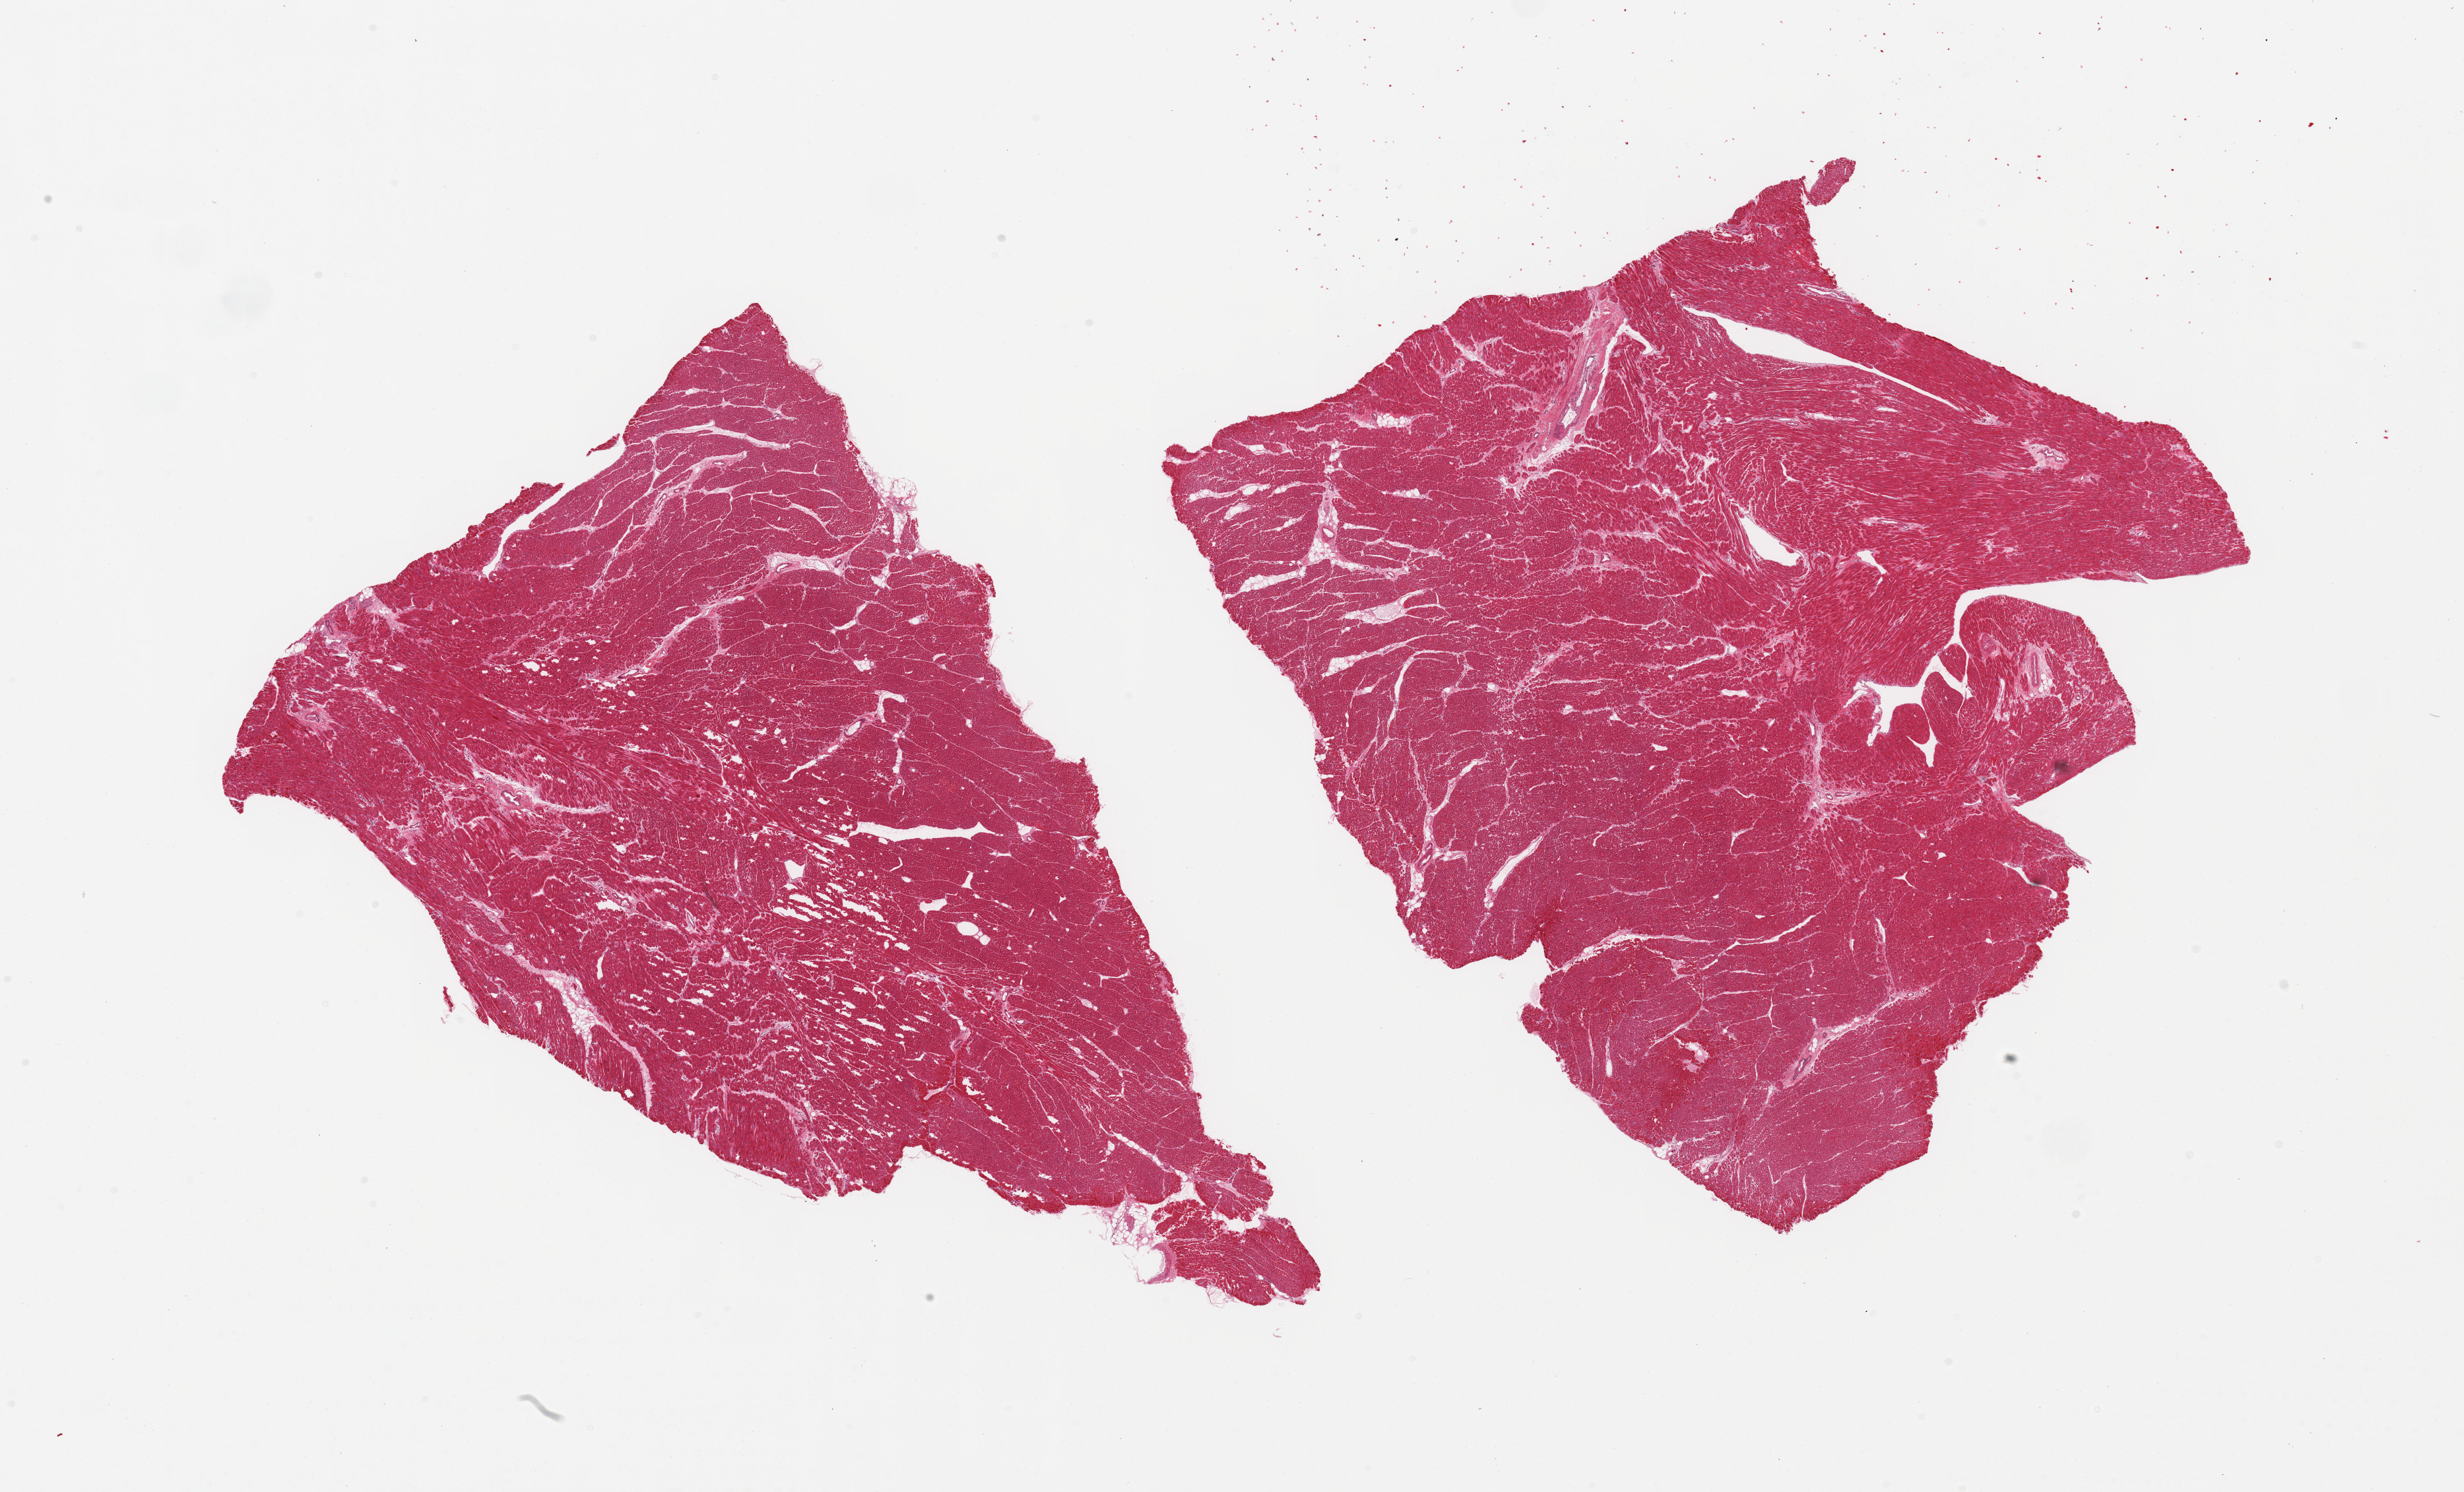
Whole-slide image, haematoxylin and eosin stain, brightfield — shown as a low-resolution overview of the whole scanned area (about 29.5 x 17.9 mm), PAXgene-fixed, paraffin-embedded tissue, target tissue: heart, donor tissue sample. Female donor.
Pathologist's review note for this sample: 2 pieces, mild interstitial fibrosis/chronic ischemic changes.